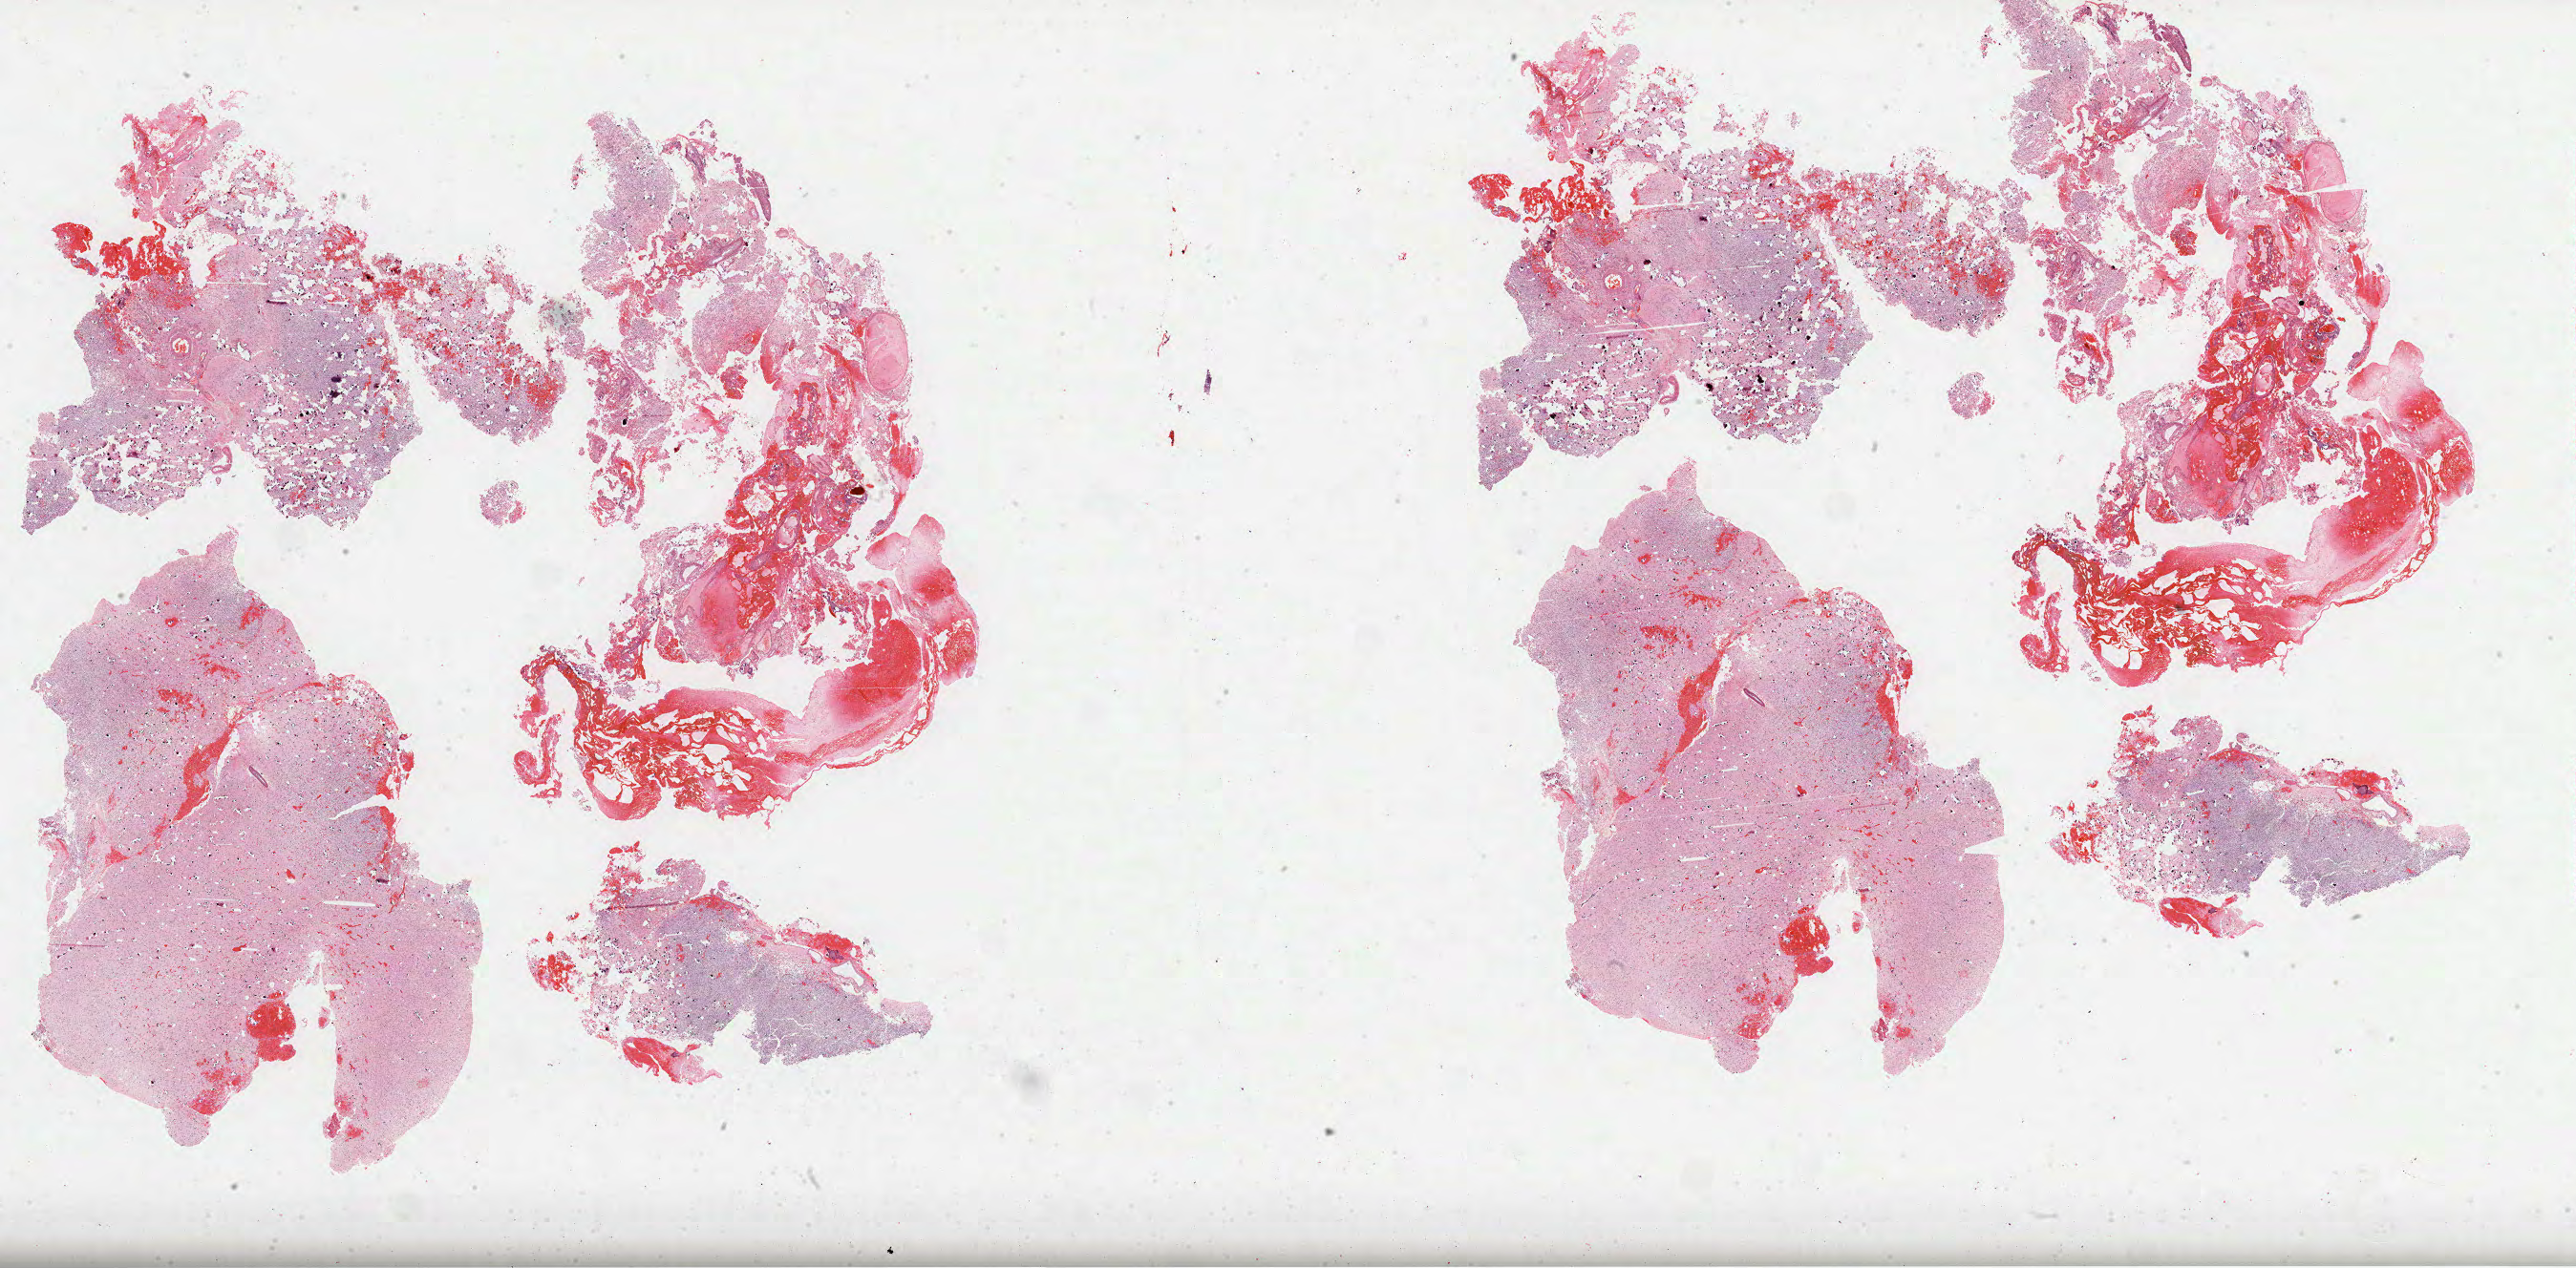
Digitized H&E tissue section (whole slide), low-resolution overview of the scanned area, about 43.5 x 21.4 mm (acquisition: 40x scan). FFPE section. Primary tumour sample from the brain. Patient: male, age at initial diagnosis 54 years. Histologic grade: G3 (poorly differentiated).
Laterality: left. Histologic diagnosis: Oligodendroglioma, anaplastic (cerebrum).